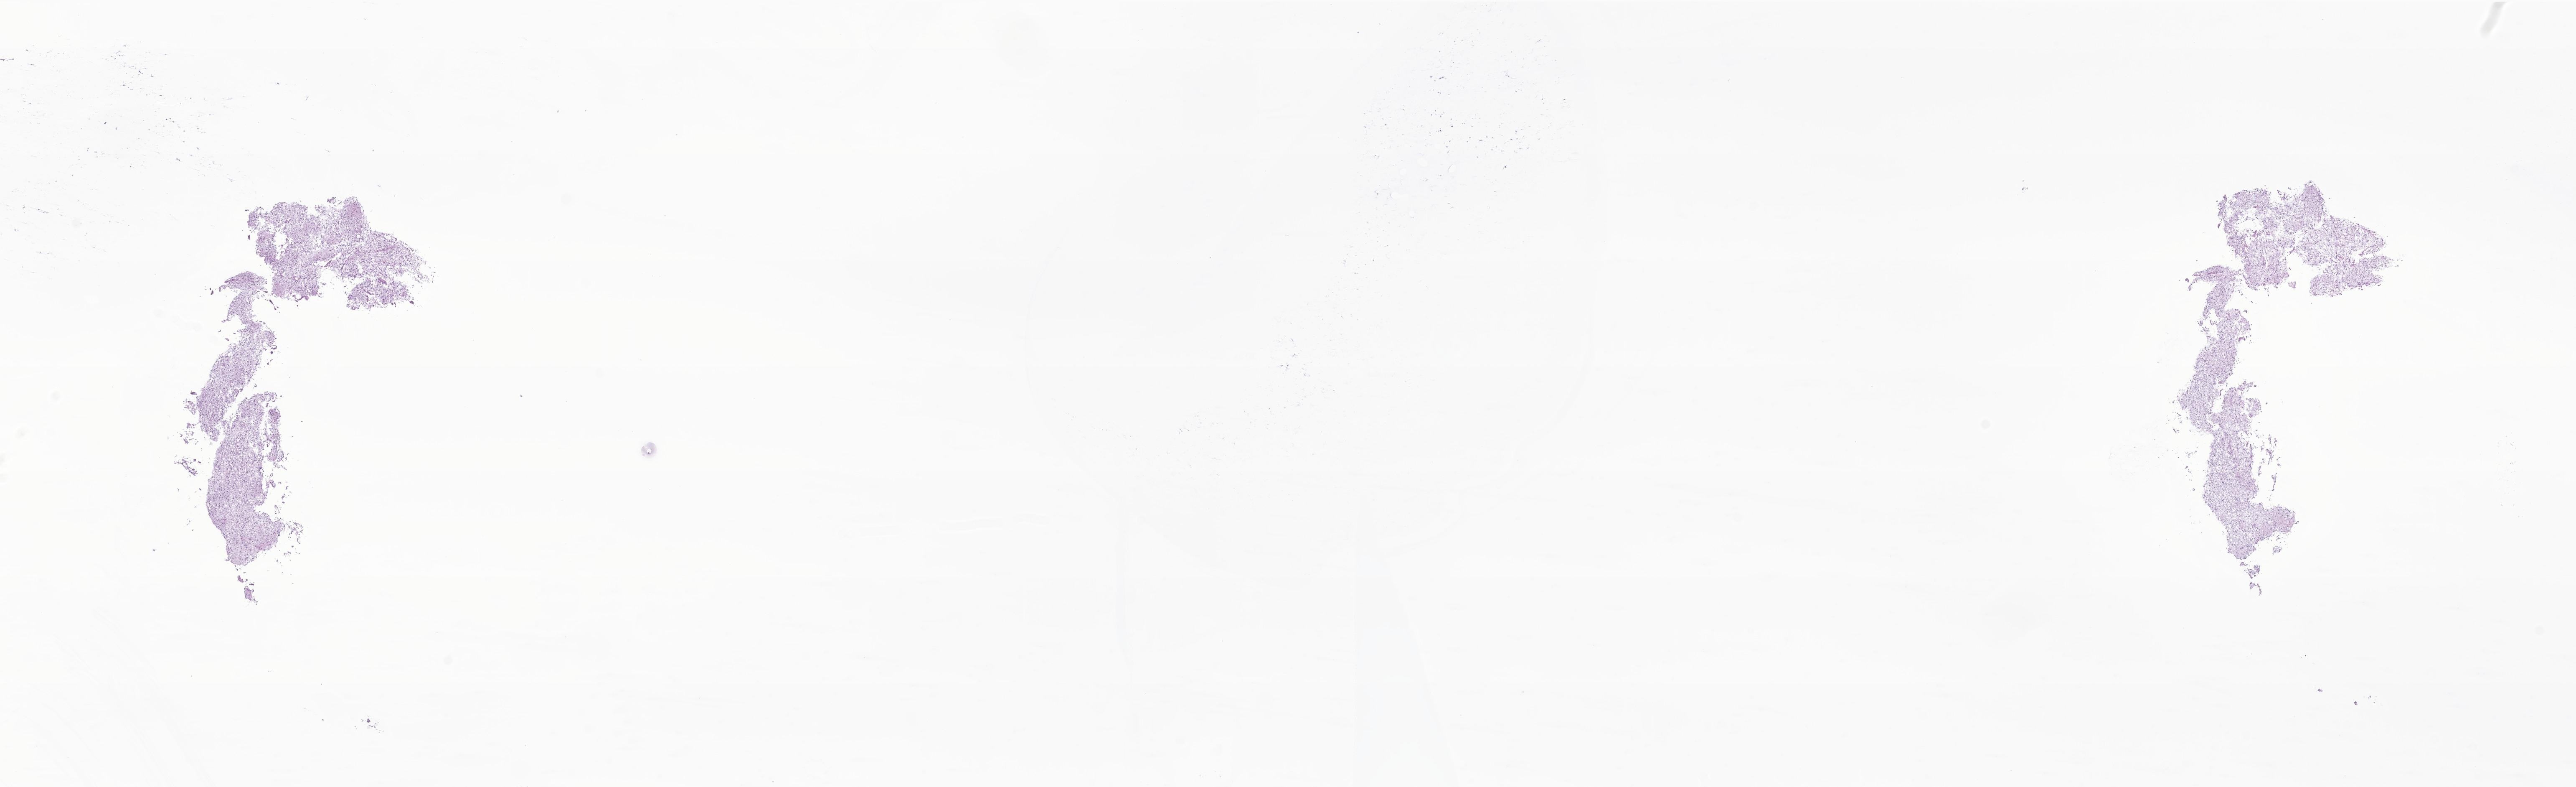
Whole-slide image, H&E stain of tumor tissue from the brain stem, low-resolution overview of the scanned area, about 26.0 x 7.9 mm. Cryosection (OCT / tissue freezing medium). Patient: male, age 40 months.
Diagnosis (ICD-O-3 morphology term): Pilocytic astrocytoma.